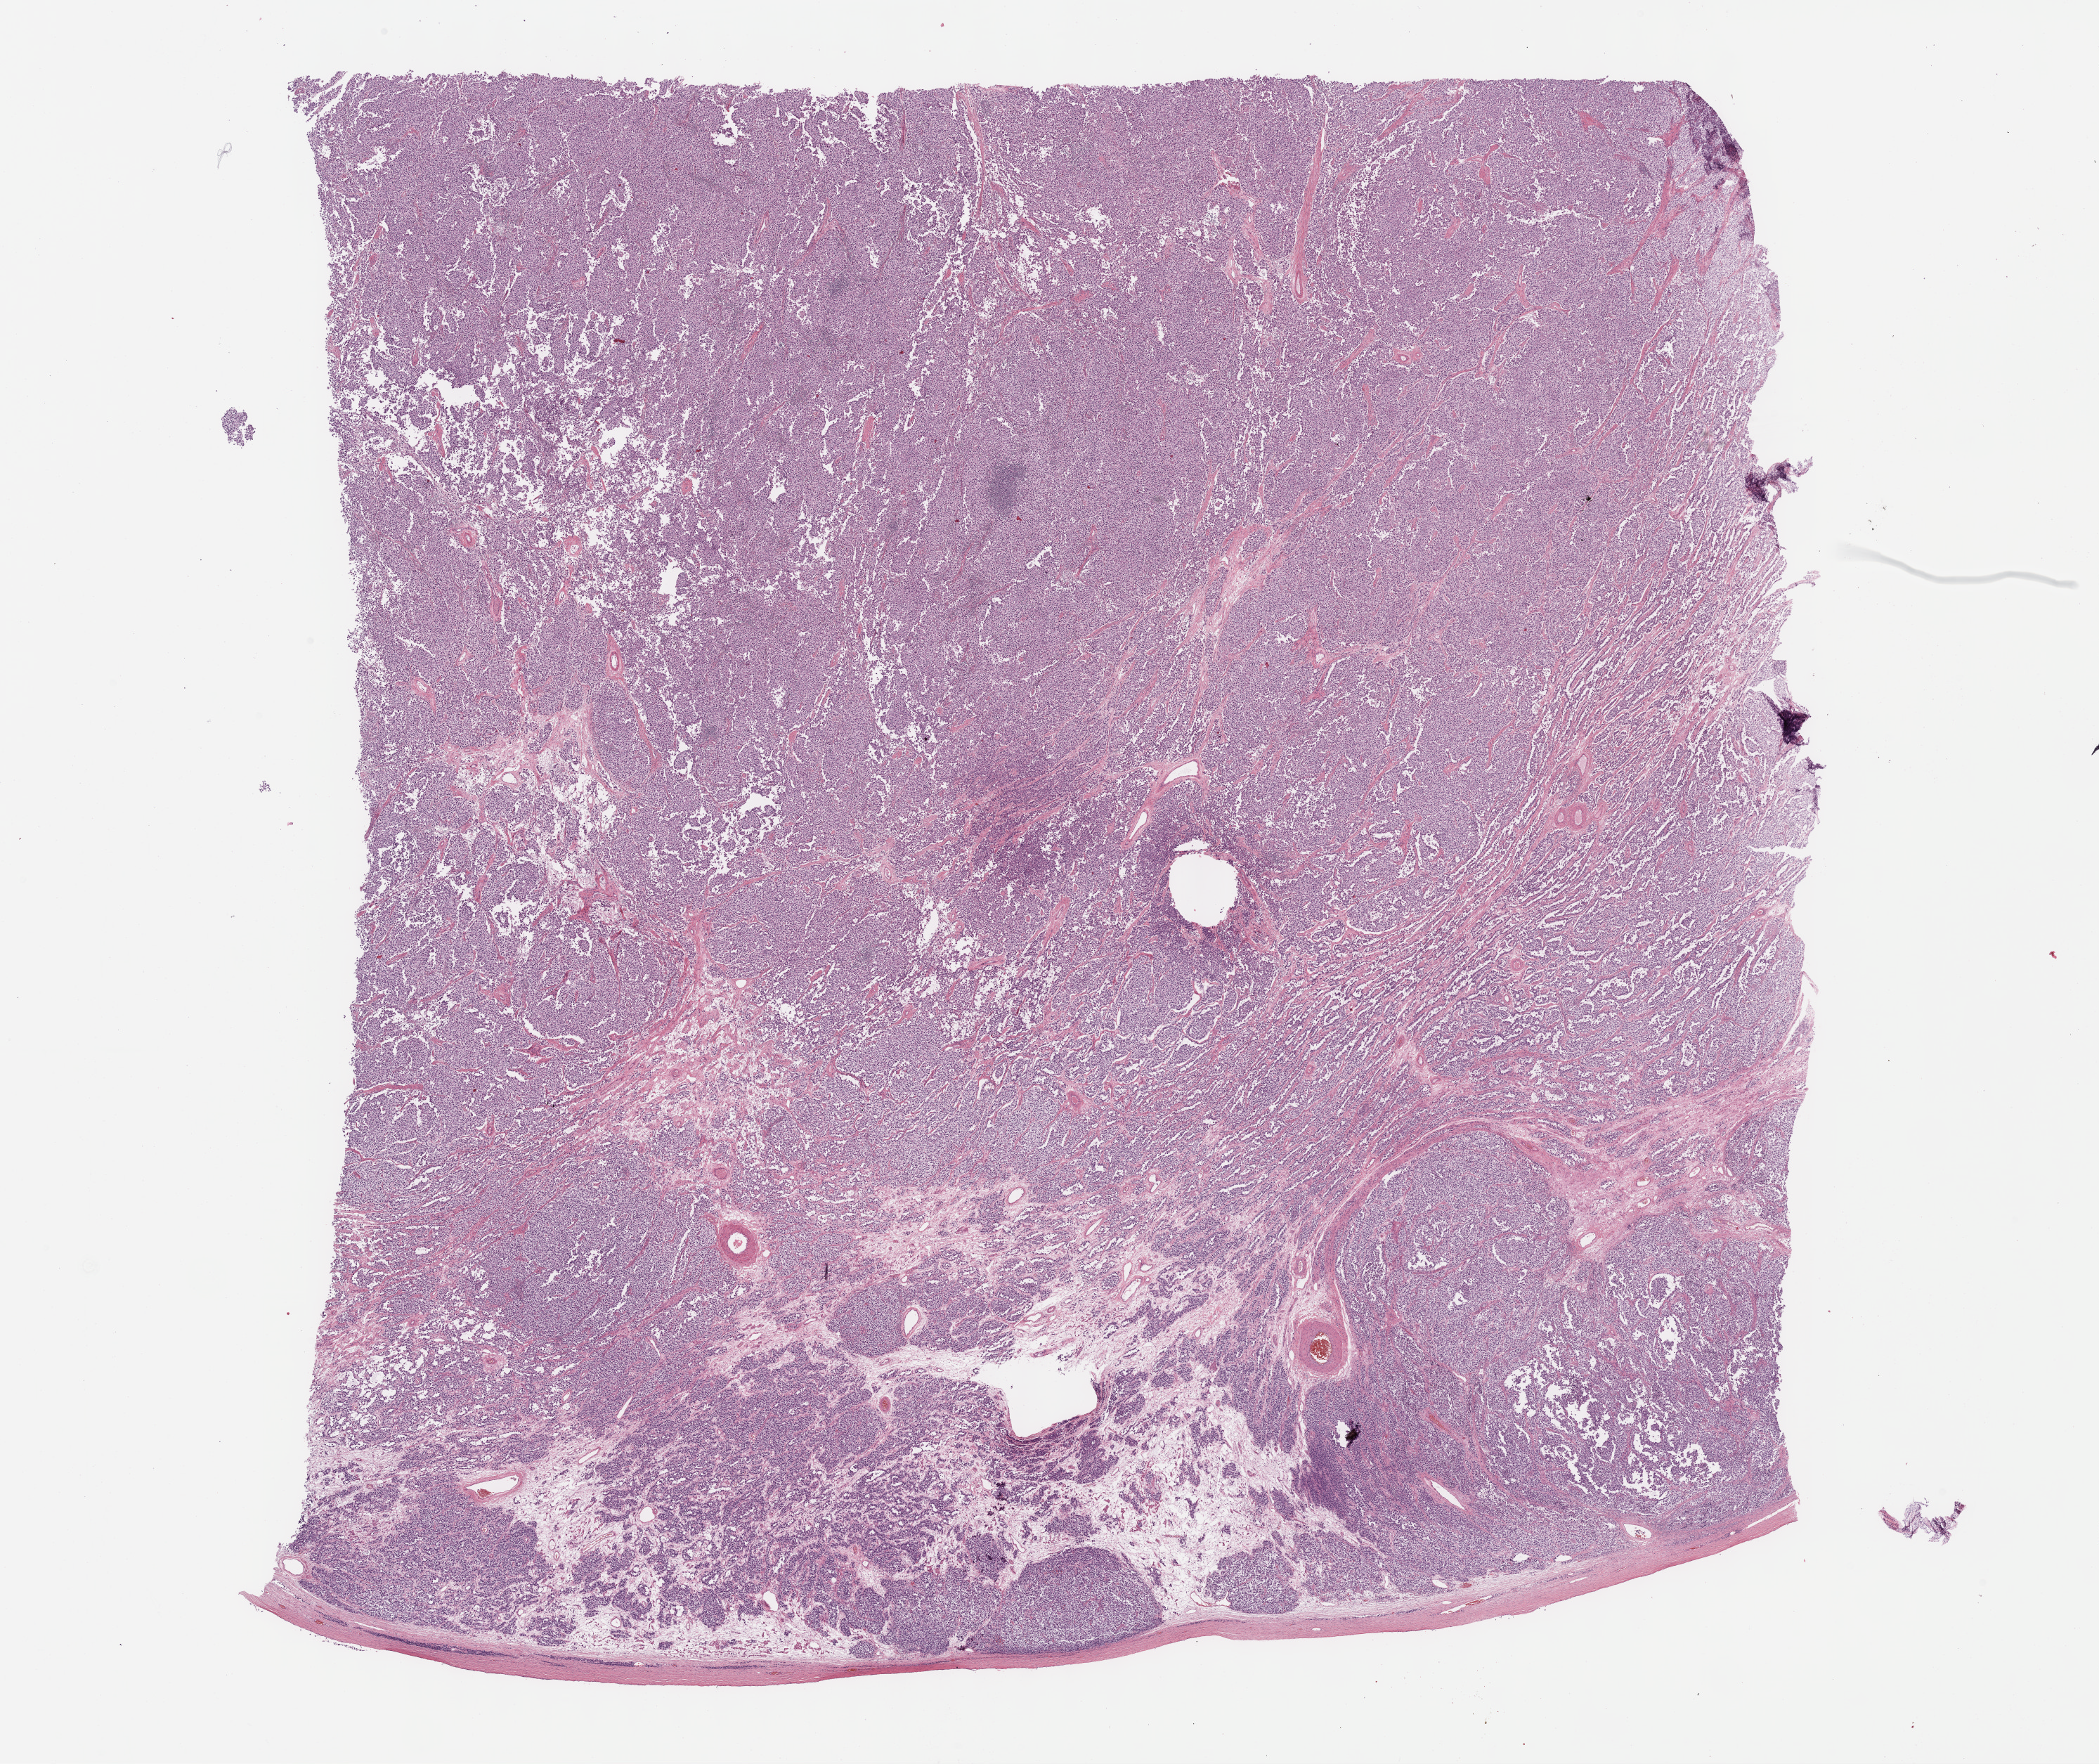
H&E whole-slide image — shown as a low-resolution overview of the whole scanned area (about 24.2 x 20.3 mm, from a 40x scan), FFPE section, primary tumour sample from the testis. Male patient; age at initial diagnosis 45 years.
Laterality: right. AJCC pathologic stage: IA. Pathologic diagnosis: Seminoma, NOS.